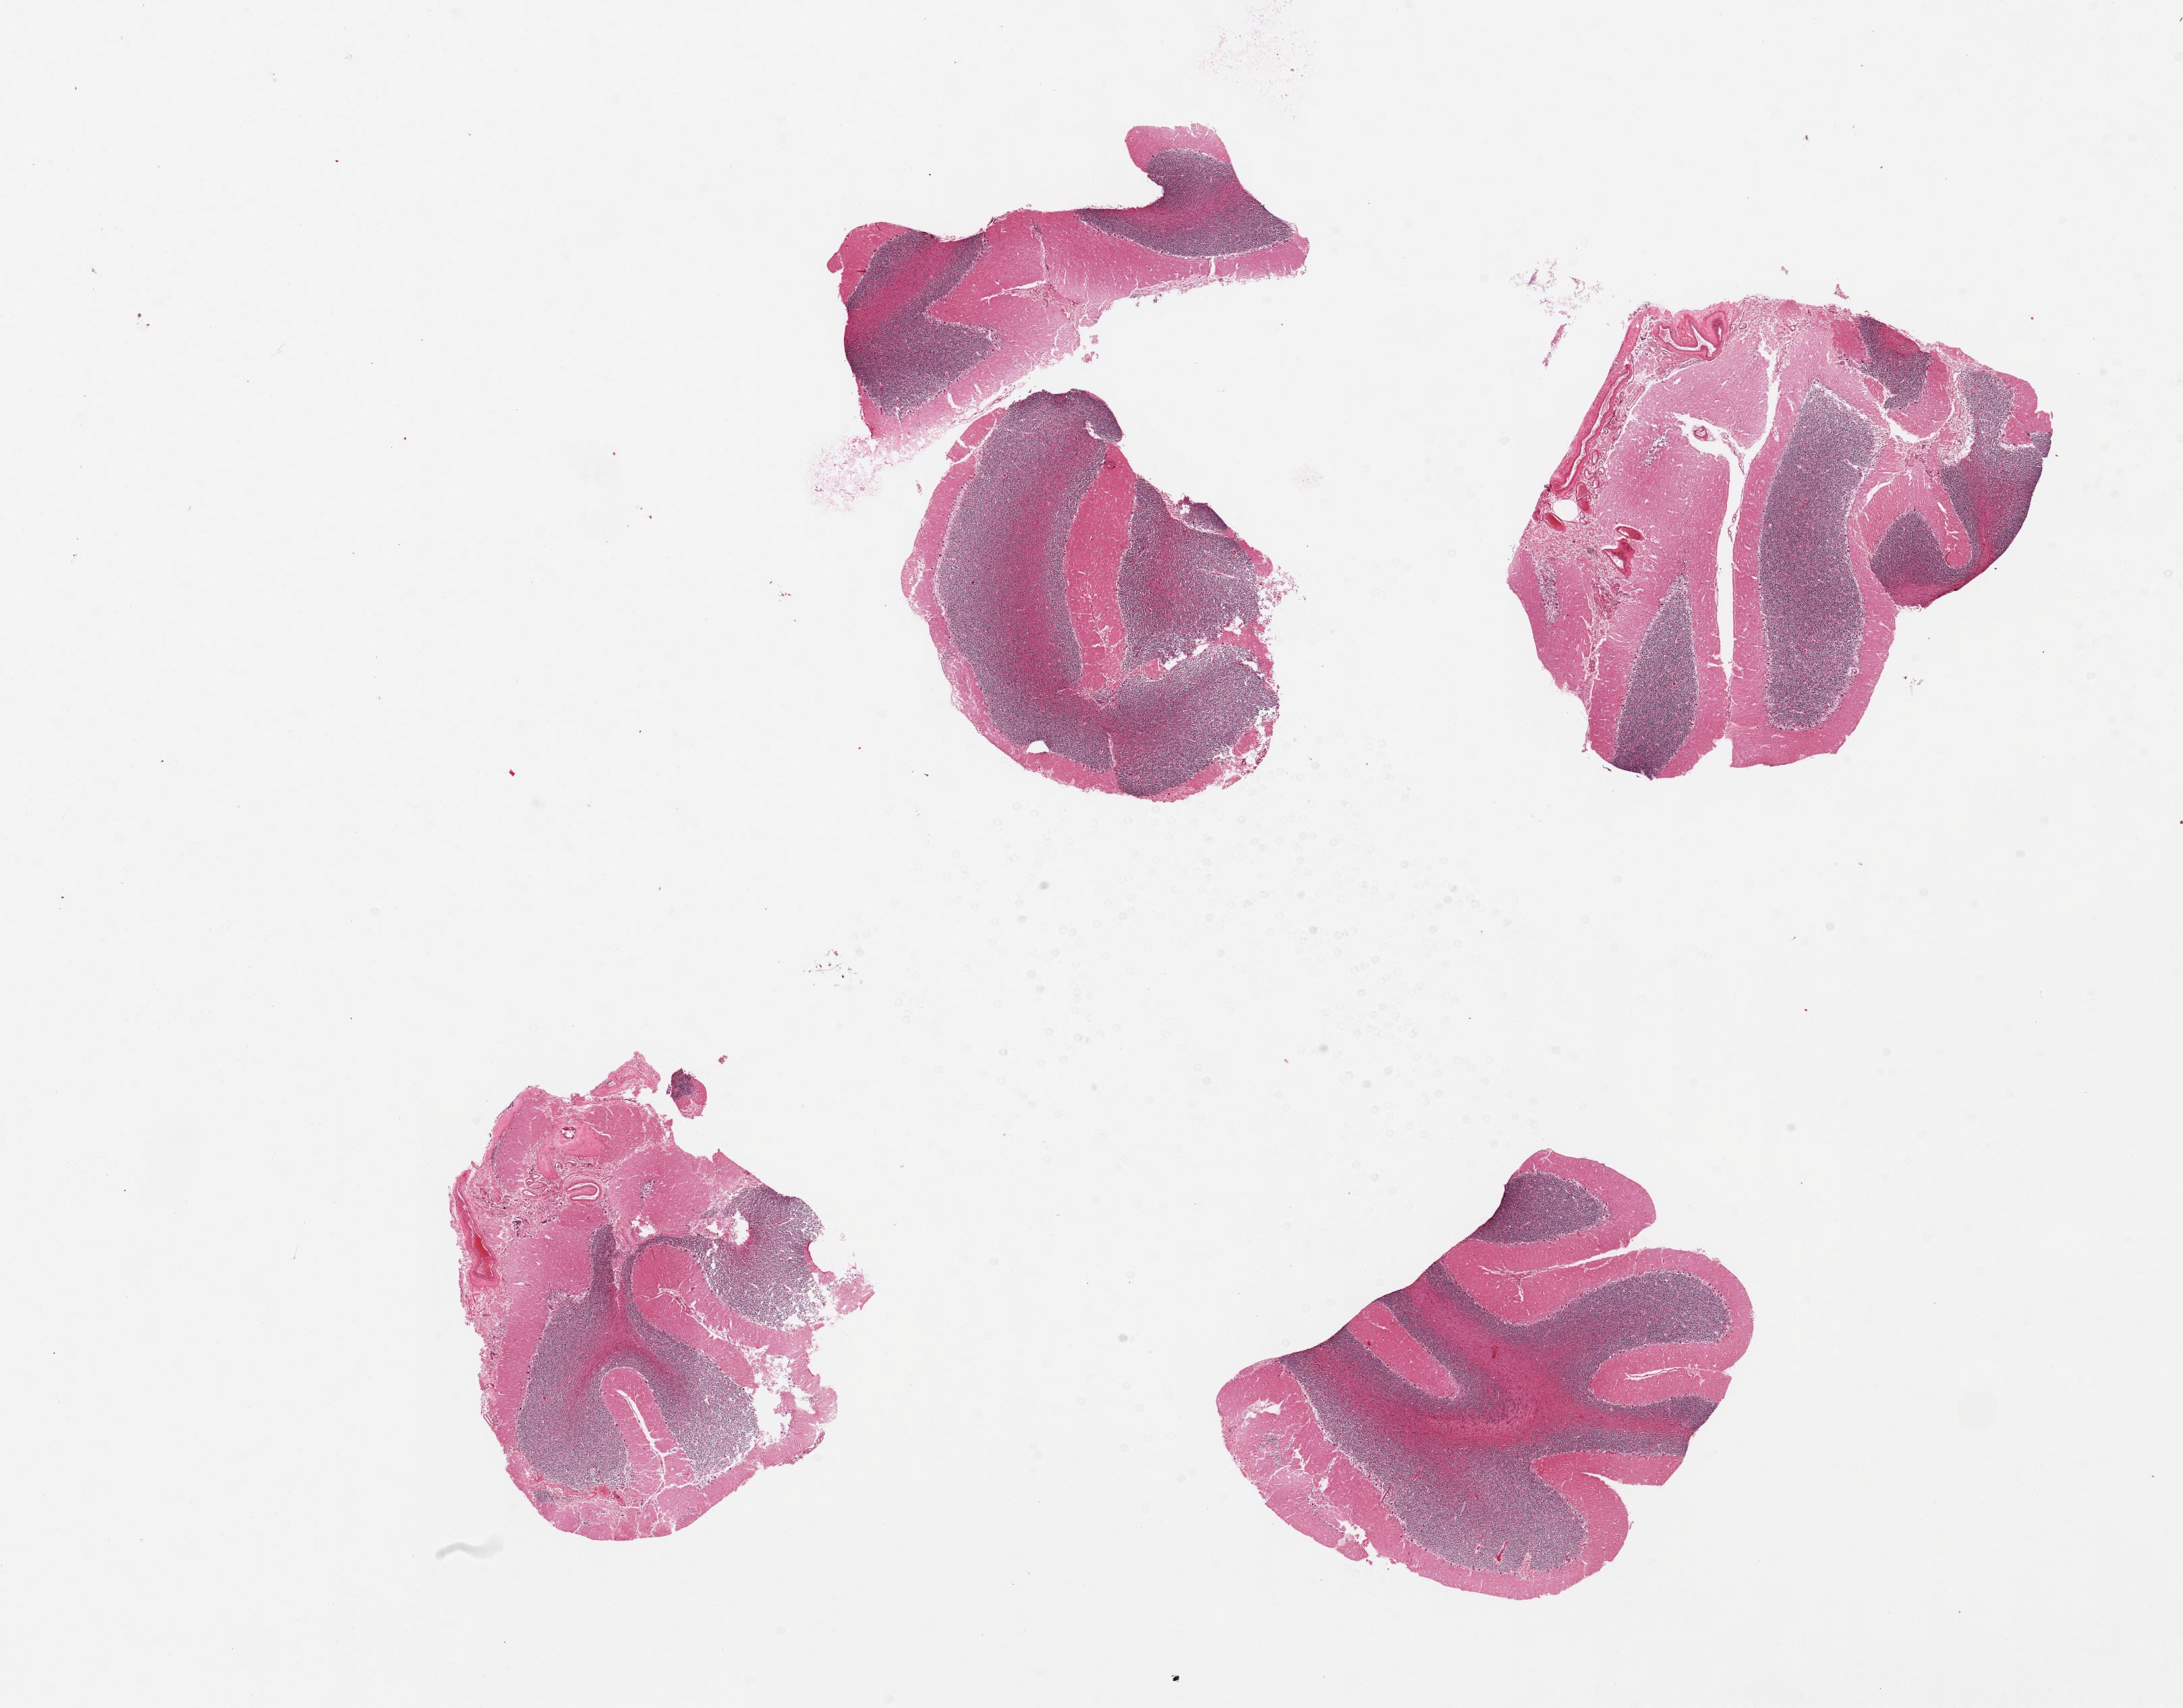
Digitized haematoxylin and eosin-stained section — shown as a low-resolution overview of the whole scanned area (about 25.6 x 20.0 mm); PAXgene-fixed paraffin-embedded (PFPE) section; target tissue: cerebellum; donor tissue sample. Donor: male.
Review note (as recorded): 4 pieces, edematous, unusually autolyzed.